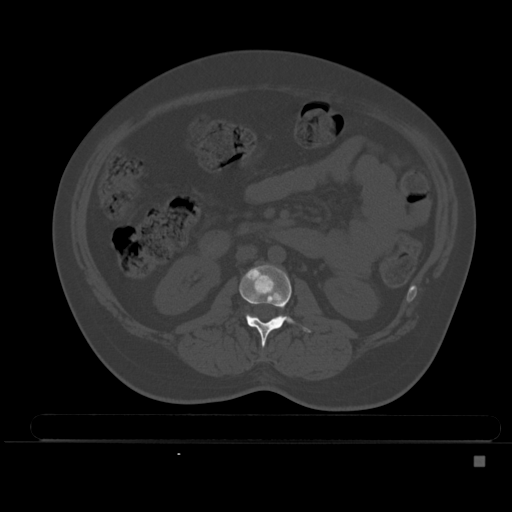
CT including the spine, one axial slice; position 170 of 495 along the scan axis; bone window (W 1800 / L 400 HU); 512 × 512 image matrix. Female patient, age 33 years. Case-level facts recorded for this patient, not image findings: primary cancer: breast; vertebrae with lytic lesions (as recorded): T1.
Structures marked on this image (semi-automatically segmented with operator editing):
- L2 vertebra: box from (x=239, y=265) to (x=312, y=347) px